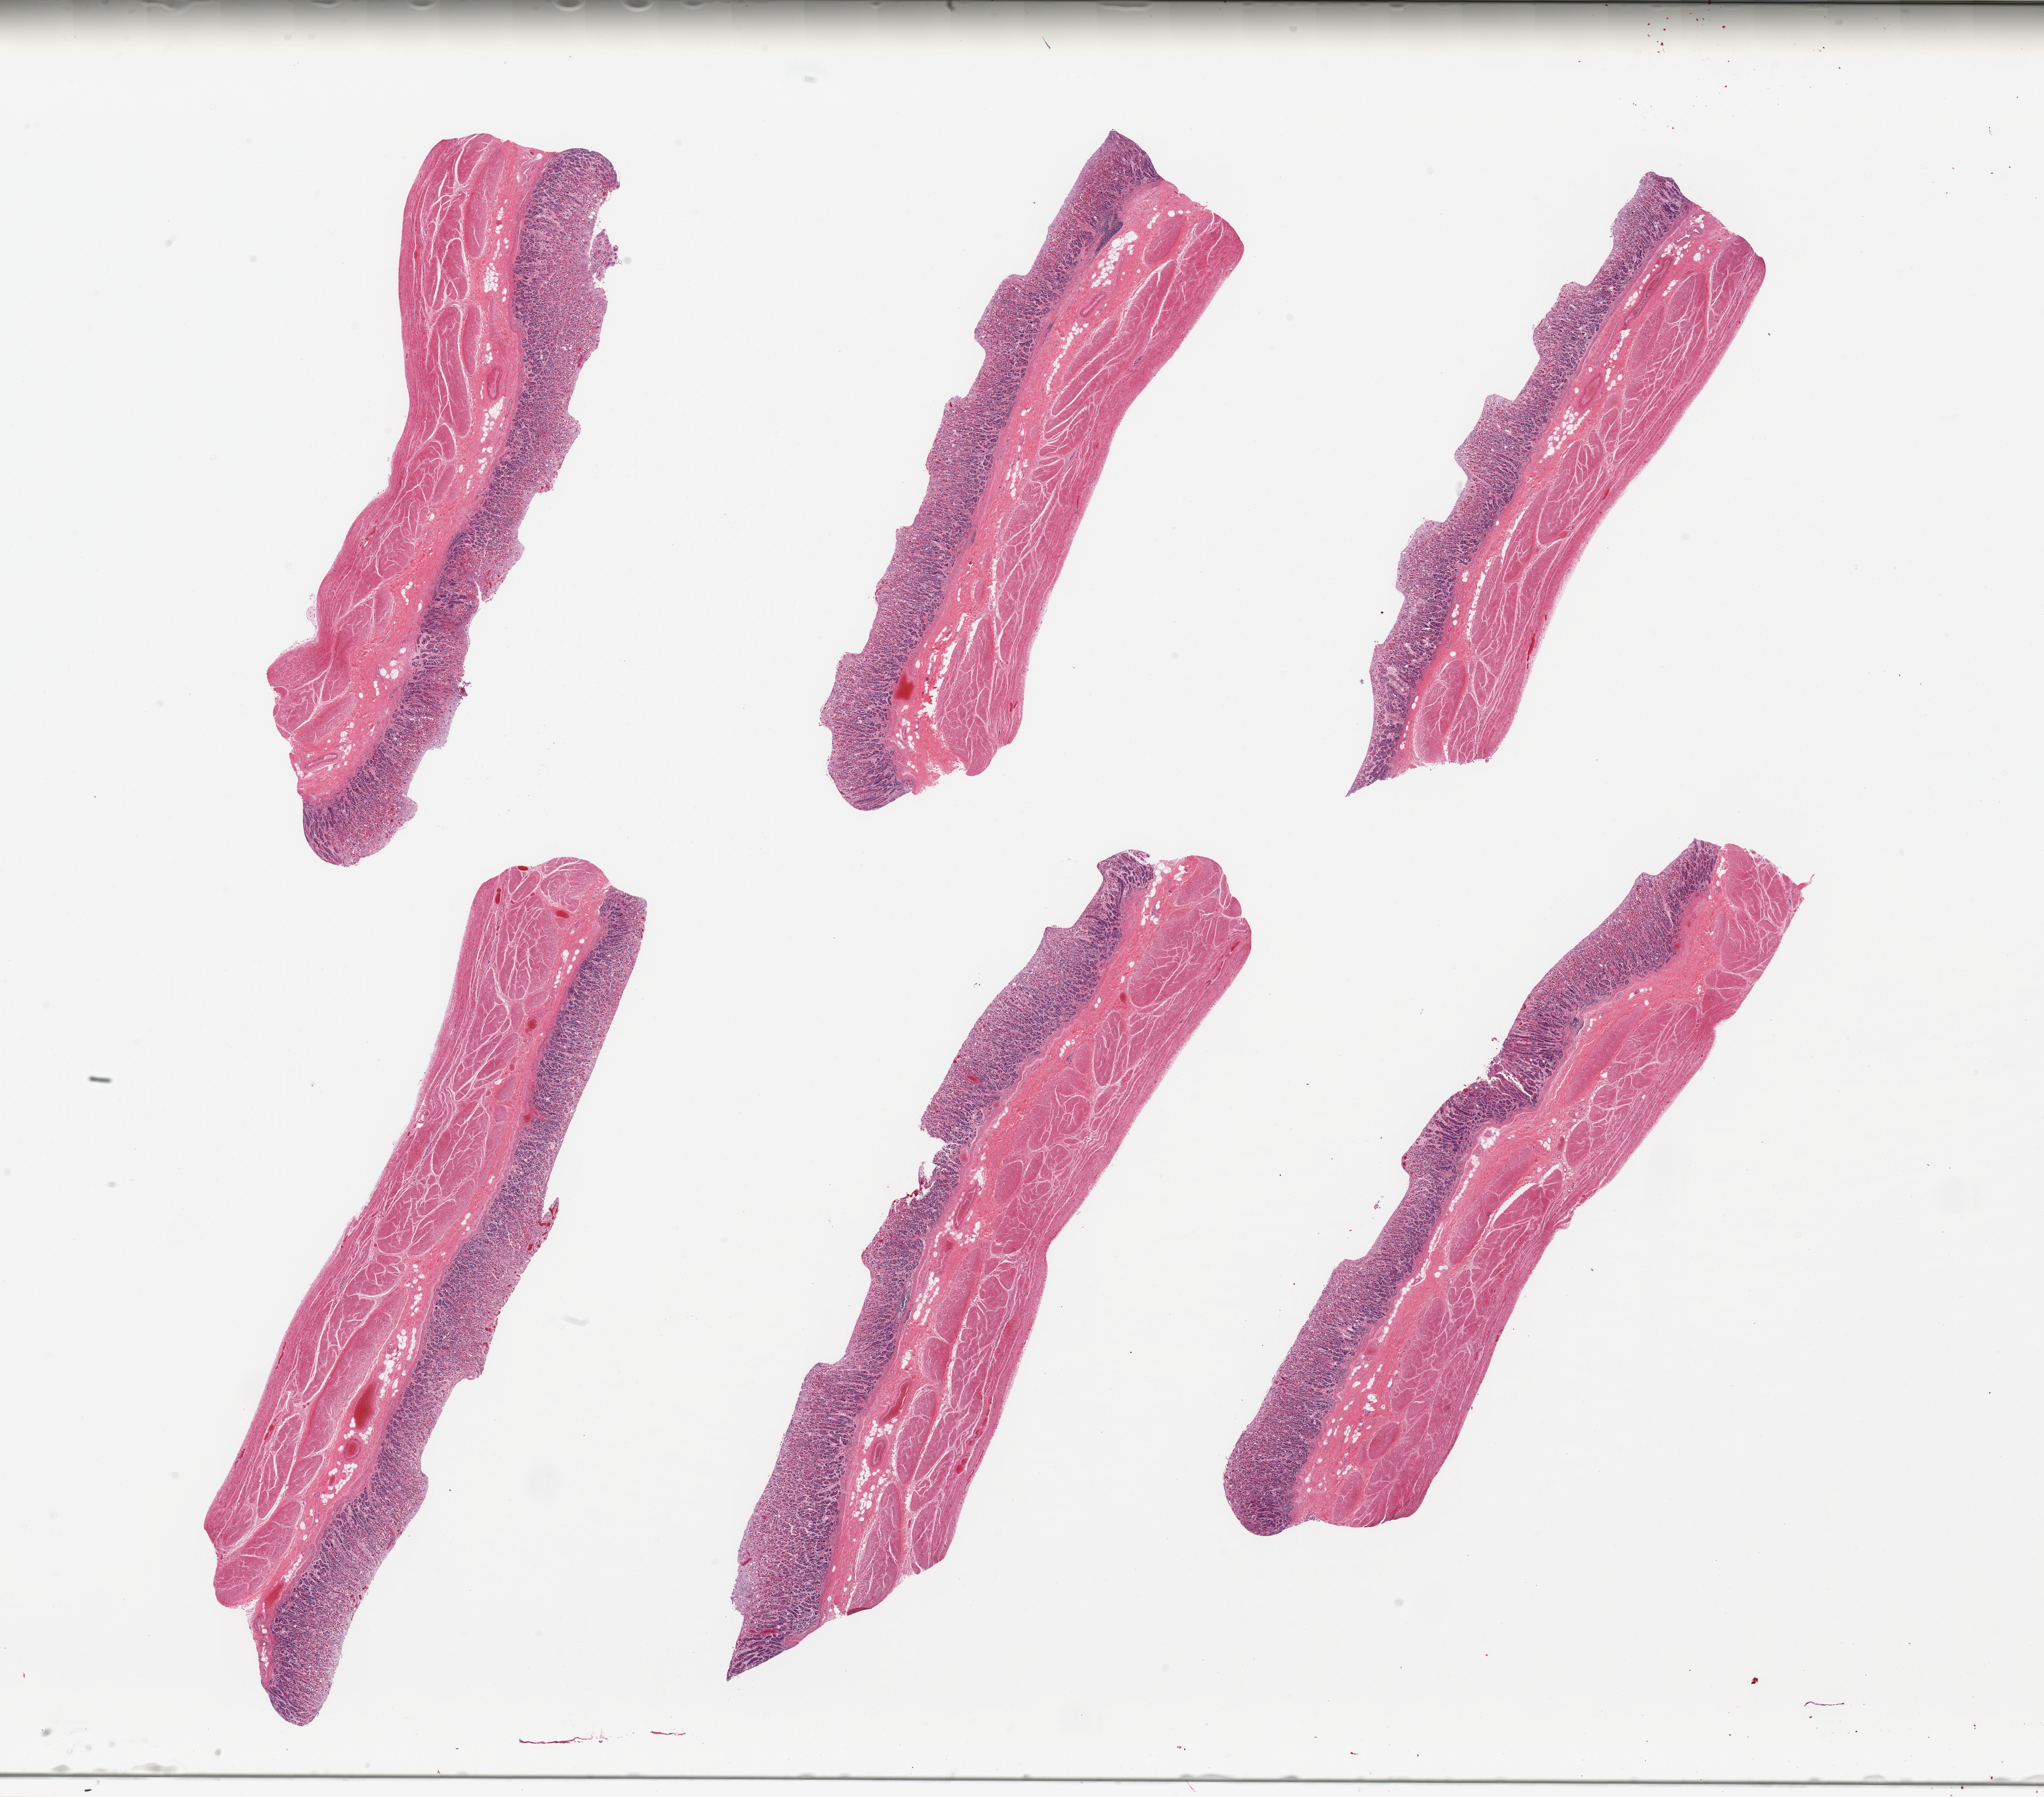
Digitized hematoxylin and eosin (H&E)-stained section — a low-resolution overview of the entire scanned area, about 27.6 x 24.2 mm (slide scanned at 20x); PAXgene-fixed paraffin-embedded (PFPE) section; sampled site (target tissue): stomach; tissue donor sample.
Review note (as recorded): 6 pieces; glands moderately autolyzed.